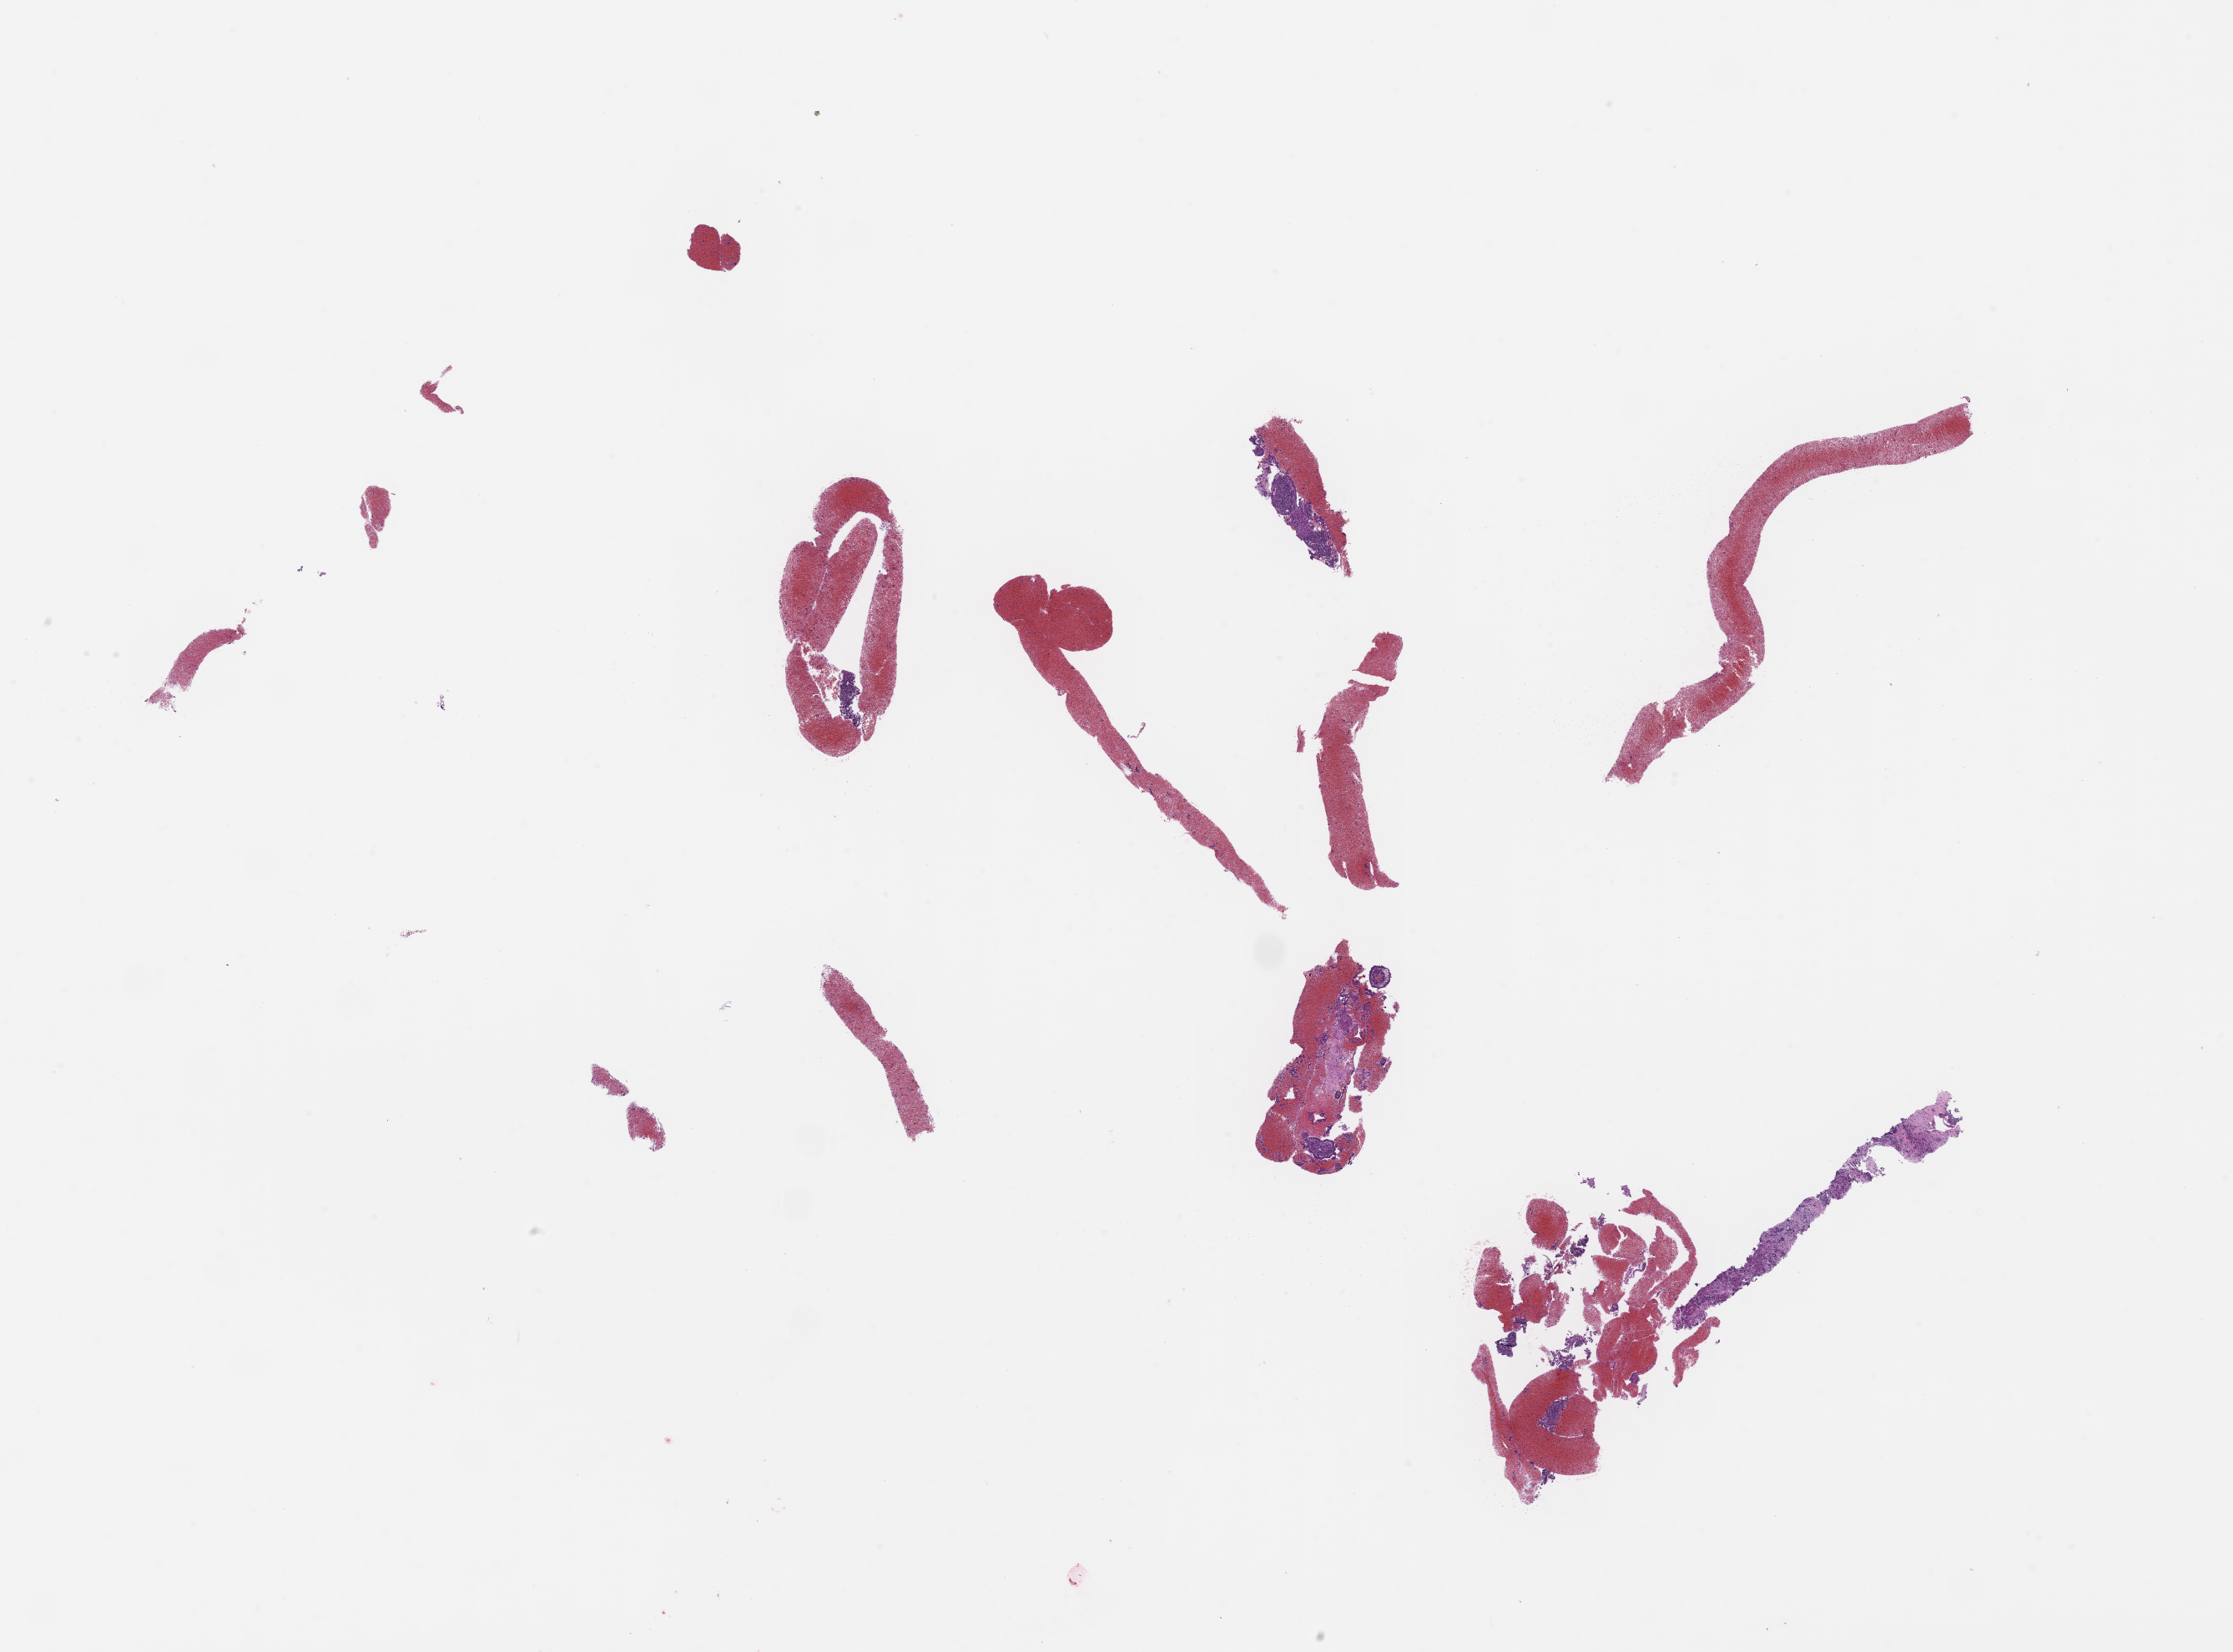
Digitized H&E-stained section — low-resolution overview of the scanned area, about 21.6 x 16.0 mm; formalin-fixed, paraffin-embedded (FFPE) tissue; site: lung; collected on treatment. Patient: male.
- this section: primary tumor
- diagnosis: Non-Small Cell Lung Carcinoma